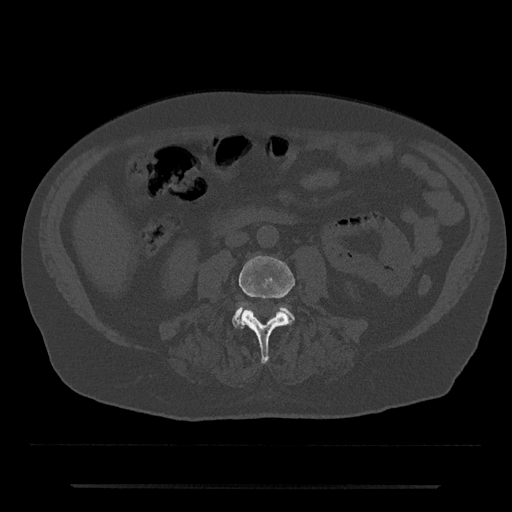
CT including the spine, one axial slice. Slice 394 of 797 in the series (ordered by position). Reconstruction kernel Br40s/3. Bone window (W 1800 / L 400 HU). 512 × 512 image matrix, field of view 434 × 434 mm. Male patient, age 80 years. From the clinical record (not read from this slice): primary cancer: prostate.
Annotated regions visible in this slice (semi-automatic segmentation, software-assisted and operator-edited):
- L3 vertebra: box from (x=238, y=256) to (x=295, y=364) px
- L4 vertebra: (x=232, y=305)–(x=294, y=328)